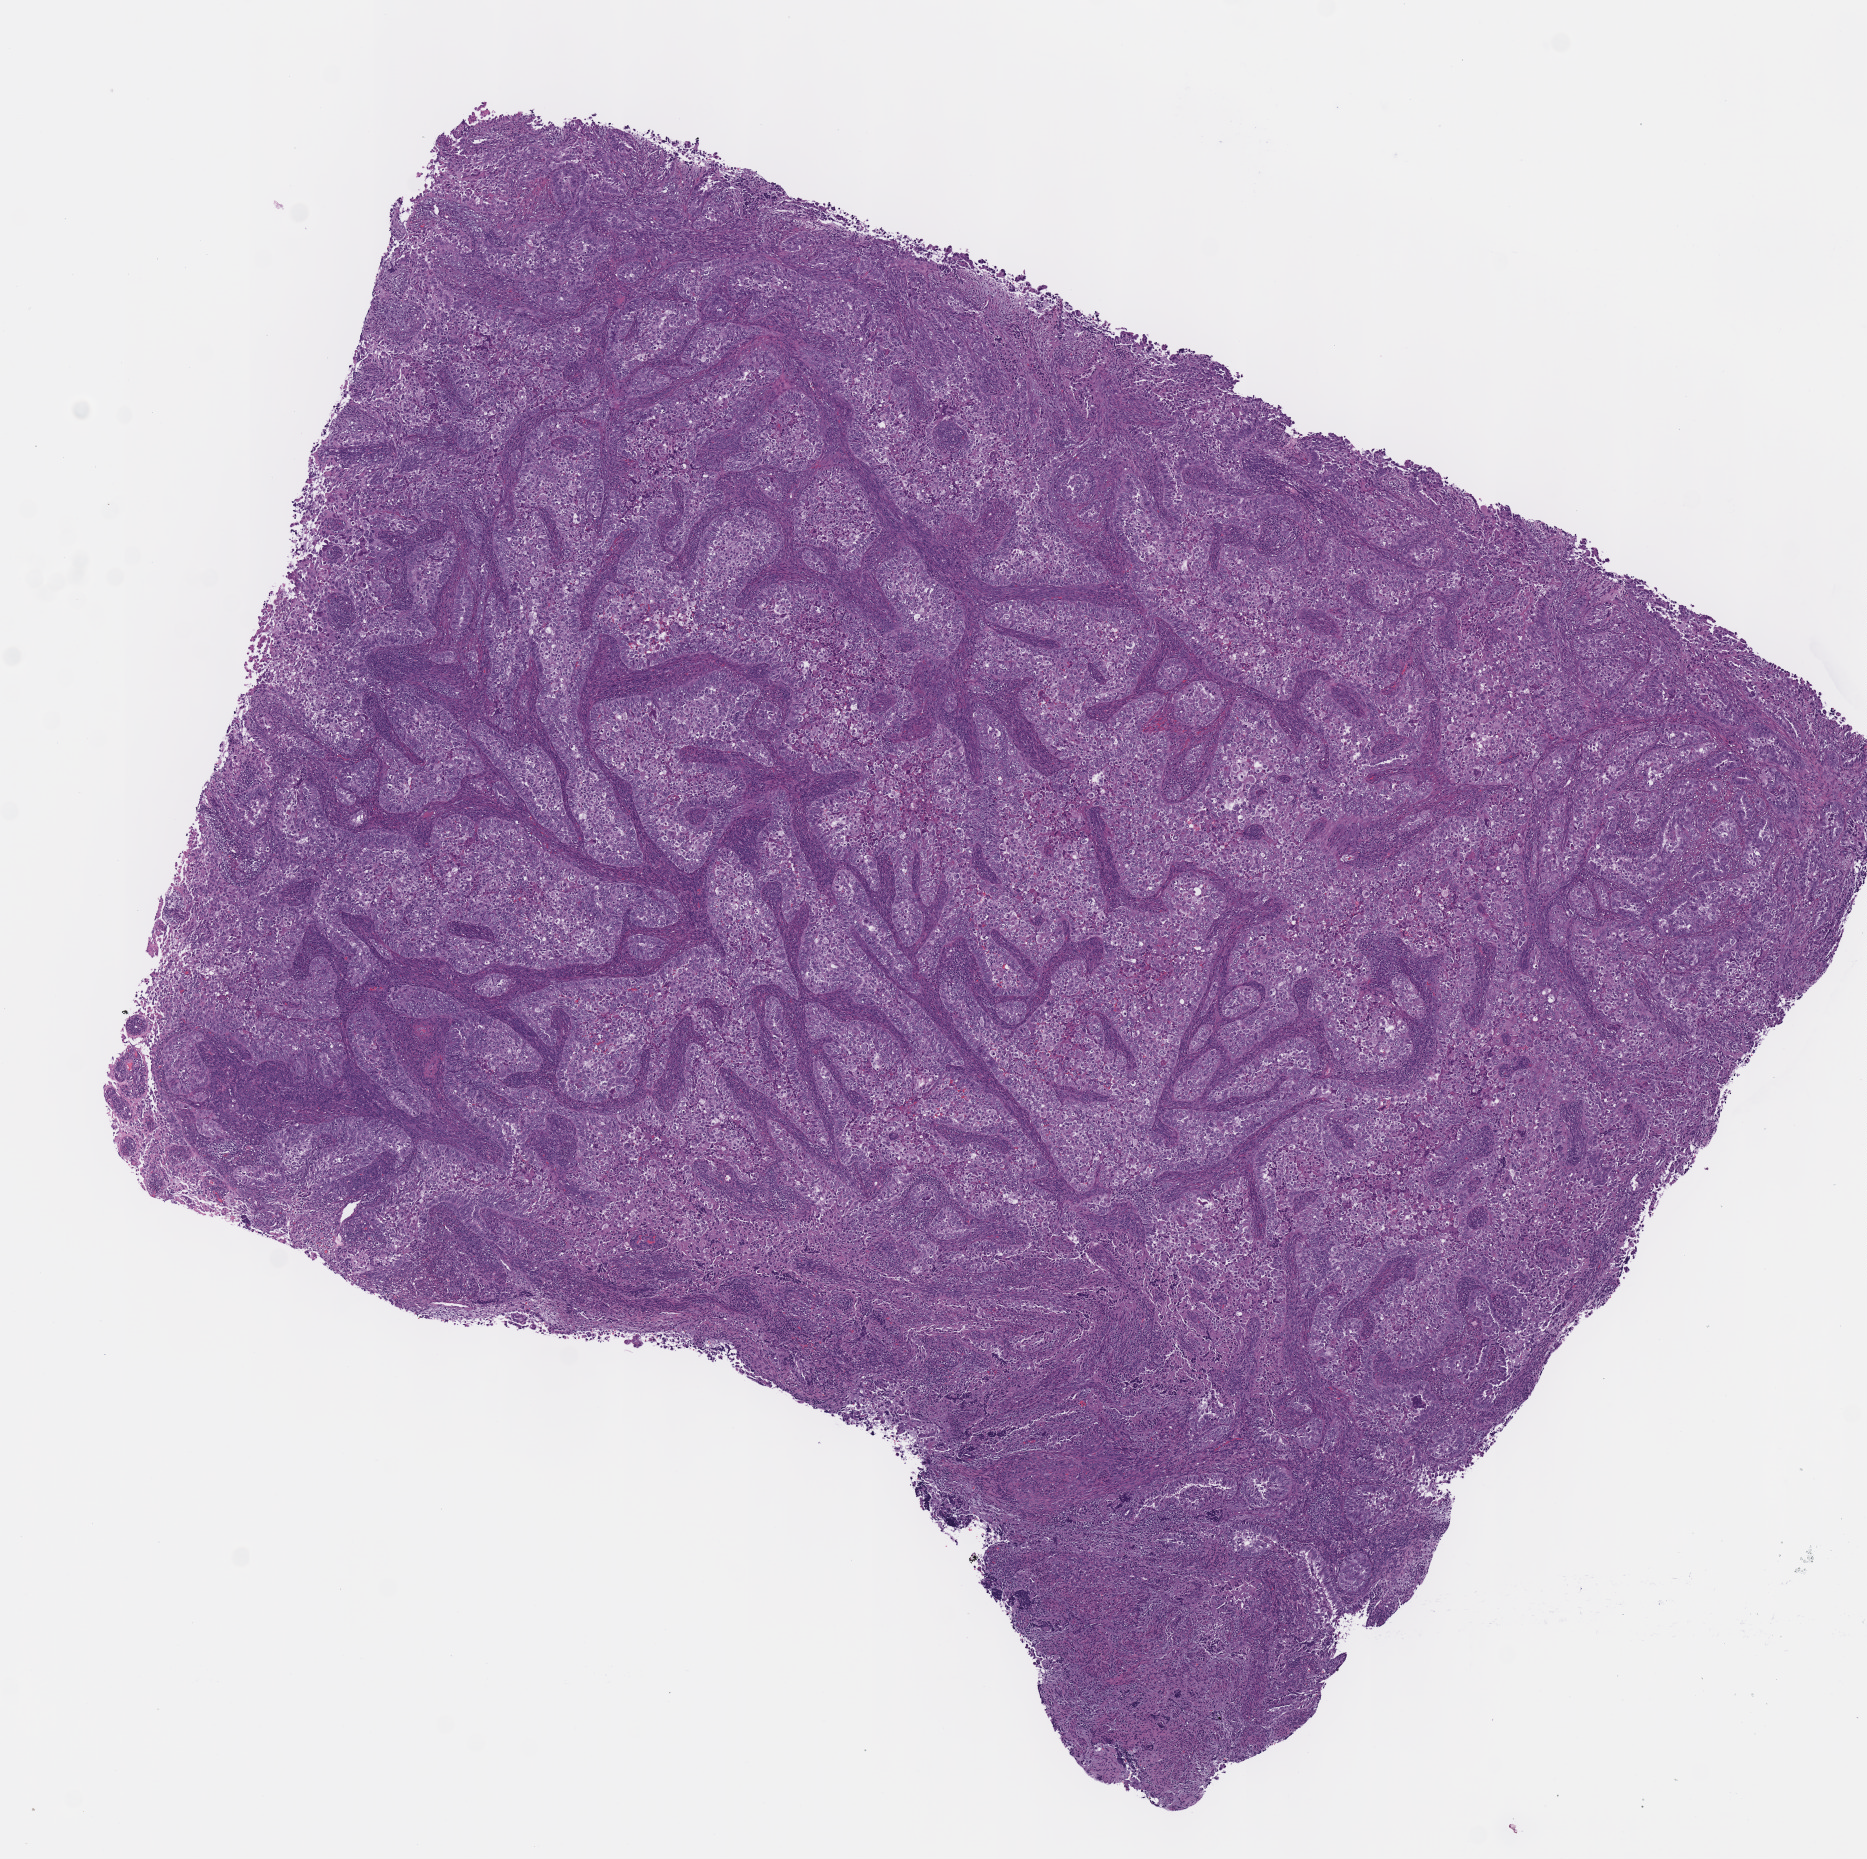
Digitized Hematoxylin and eosin (H&E) stained tissue section (whole slide), low-resolution overview of the scanned area, about 7.3 x 7.3 mm (slide scanned at 40x). Formalin-fixed paraffin-embedded (FFPE) diagnostic section. Uterus, primary tumour sample. Female patient; age at initial diagnosis 77 years. Histologic grade: G3 (poorly differentiated).
FIGO stage: IB. Diagnosis: Endometrioid adenocarcinoma, NOS (endometrium).